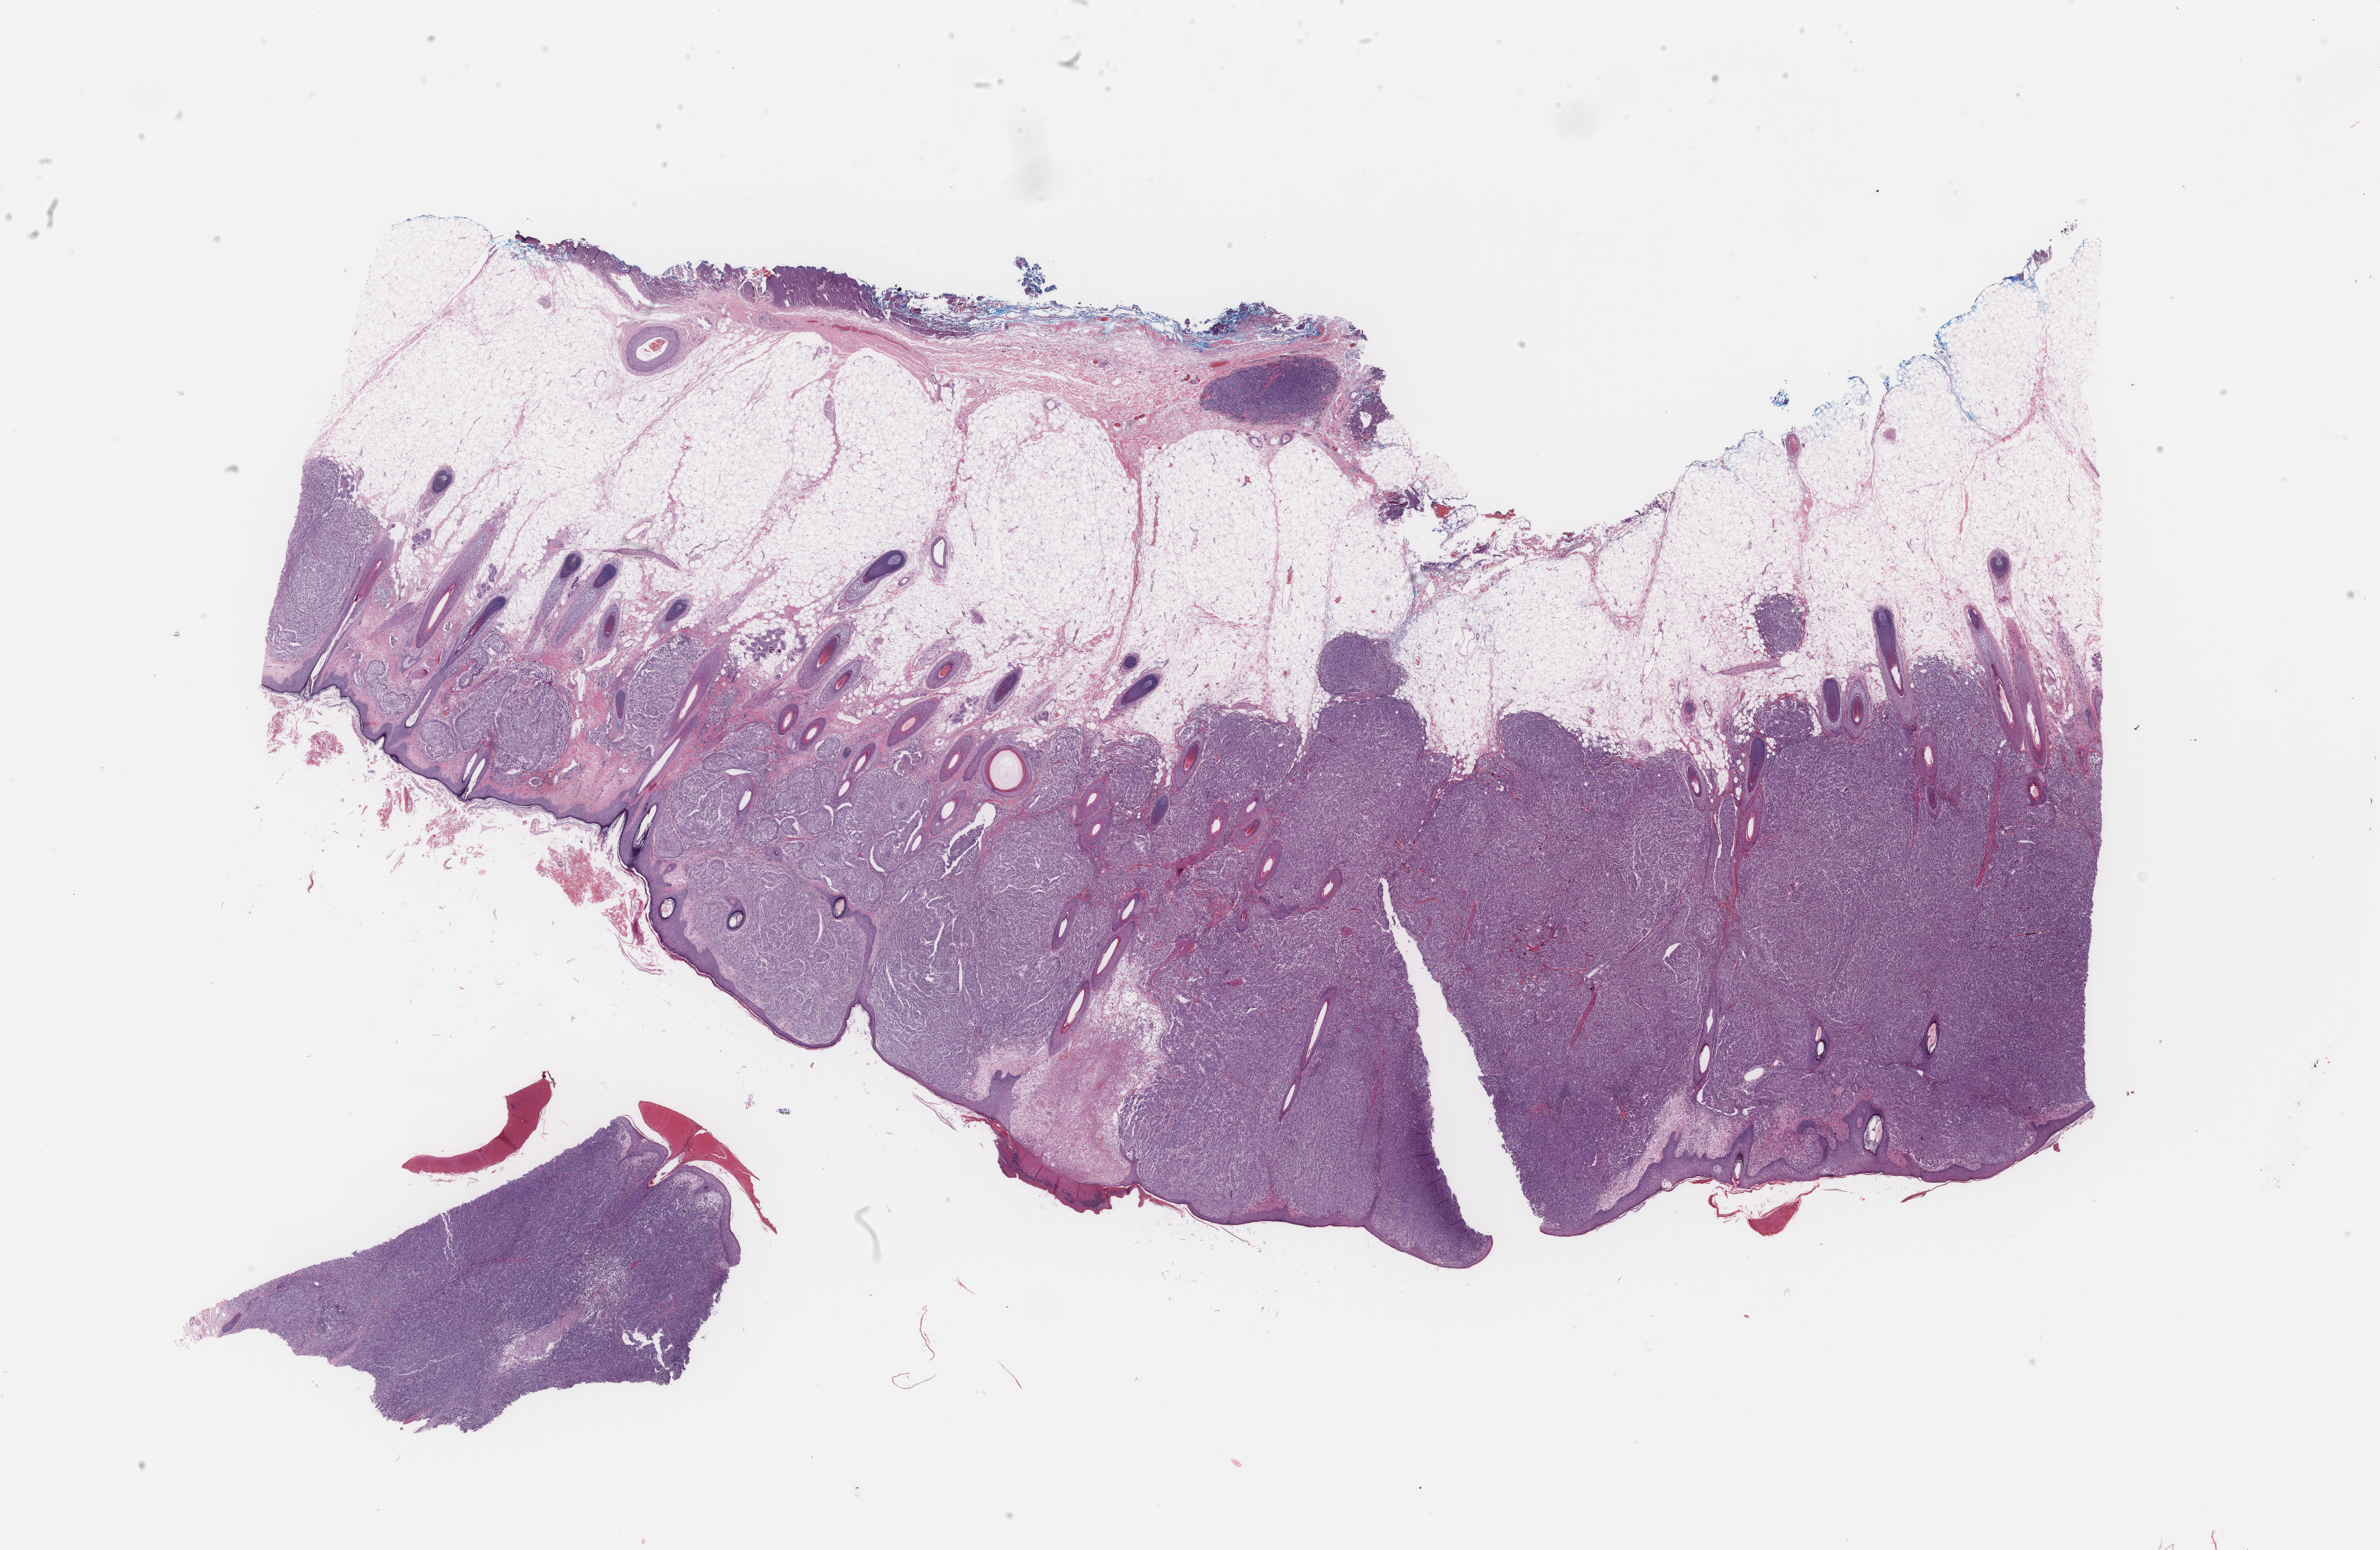
Whole-slide histology image, Hematoxylin and eosin (H&E) stained, whole scanned area (about 27.6 x 18.0 mm, slide scanned at 40x) shown as a low-resolution overview. FFPE section. Skin, primary tumour sample. Female, age 79 years at initial diagnosis.
Histologic diagnosis: Malignant melanoma, NOS.